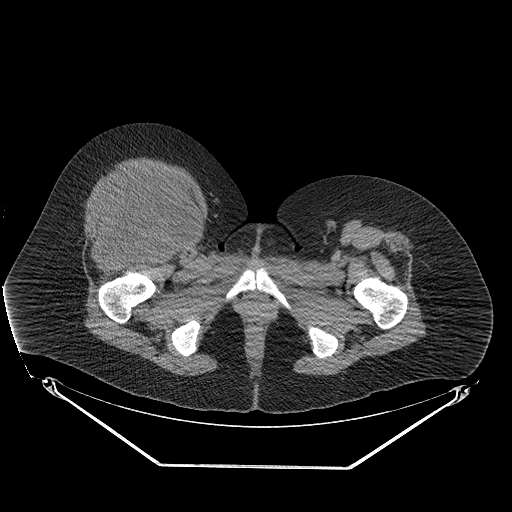
CT of an extremity soft-tissue mass (from a PET/CT study), one axial slice. Slice 57 of 267 in the series (ordered by position). Reconstruction kernel STANDARD. 140 kVp. Soft-tissue window (W 400 / L 40 HU). 512 × 512 image matrix, field of view 500 × 500 mm. Female patient. From the clinical record (not read from this slice): histological type: malignant solitary fibrous tumor; grade: intermediate; site of the primary tumour: right thigh.
Annotated regions visible in this slice (expert contour drawn on MRI and transferred to this co-registered scan by the dataset authors):
- gross tumour volume including surrounding oedema: box from (x=89, y=167) to (x=193, y=241) px
- gross tumour volume (mass): (x=89, y=171)–(x=190, y=241)